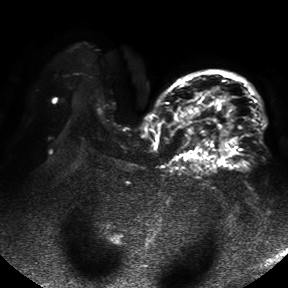
Breast MRI, one axial slice. Diffusion-weighted series; image 2 of 4 stored at this slice position (different b-values; order by instance number). 1.5 T. 4 mm slice thickness. 288 × 288 image matrix, field of view 390 × 390 mm. Female patient.
Outlined on this slice (expert manual segmentation):
- tumour on diffusion-weighted imaging: bounding box [x1, y1, x2, y2] px = [169, 100, 238, 159]